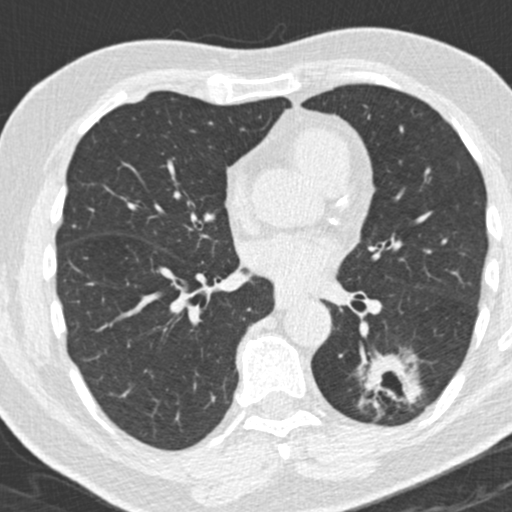
Low-dose screening chest CT, one axial slice. Reconstruction kernel B30f. 120 kVp. Lung window (W 1500 / L -600 HU). 512 × 512 image matrix, field of view 300 × 300 mm.
Outlined on this slice (outlined manually by an expert reader):
- lesion 1 (tumor, lower lobe of left lung): bounding box [x1, y1, x2, y2] px = [365, 356, 421, 402]